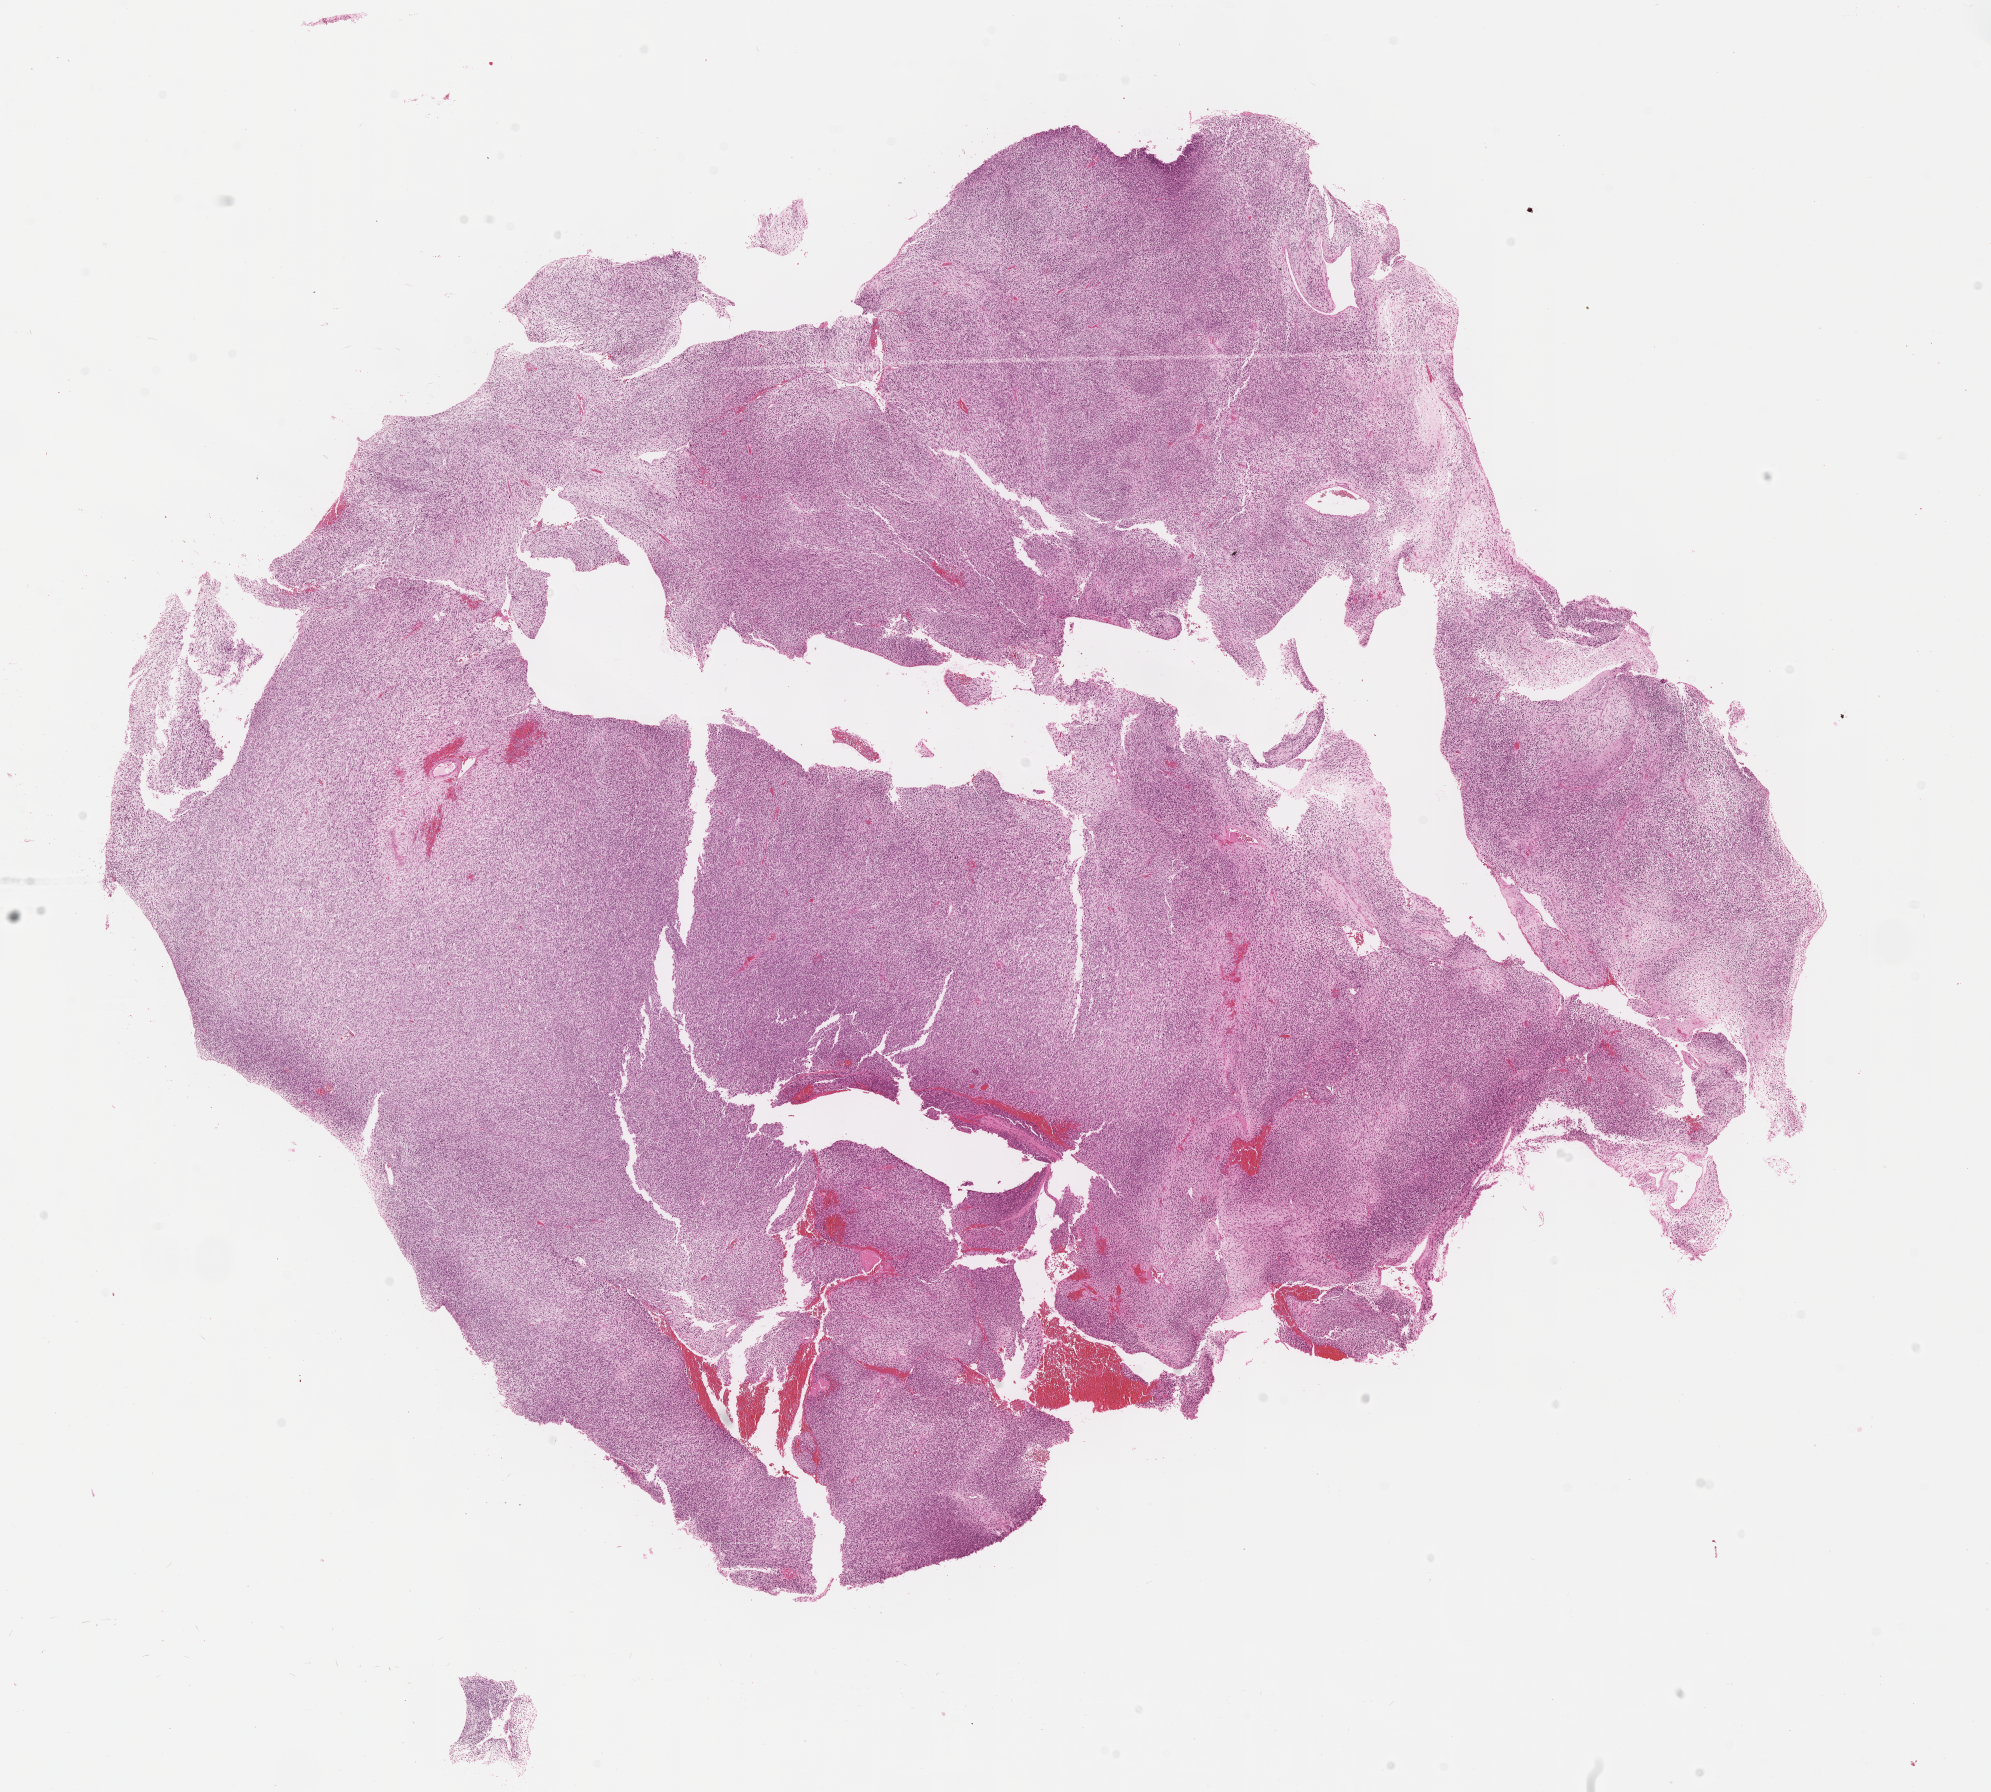
Digitized H&E-stained section of tumor tissue — whole scanned area (about 16.1 x 14.5 mm) shown as a low-resolution overview. FFPE section. Site: pelvis. Patient: female, age 5.2 years at diagnosis.
Metastatic status at presentation (as recorded): non-metastatic. Diagnosis: rhabdomyosarcoma; histological classification: embryonal rhabdomyosarcoma. Stage (as recorded): 3.